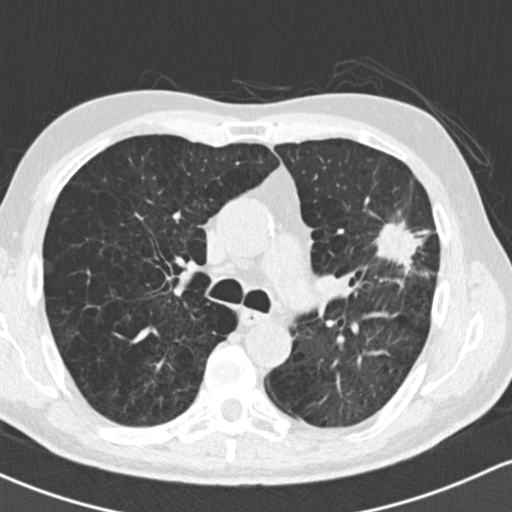
Low-dose screening chest CT, one axial slice; position 98 of 162 along the scan axis; 120 kVp; lung window (W 1500 / L -600 HU); 2 mm slice thickness; 512 × 512 image matrix, field of view 318 × 318 mm.
Annotated regions visible in this slice (outlined manually by an expert reader):
- lesion 1 (tumor, upper lobe of left lung): bounding box (x1, y1, x2, y2) in pixels: (374, 222, 420, 275)